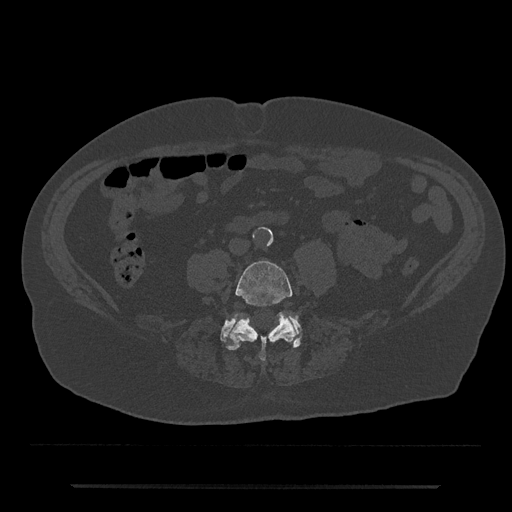
CT including the spine, one axial slice; position 336 of 797 along the scan axis; reconstruction kernel Br40s/3; bone window (W 1800 / L 400 HU); 0.5 mm slice thickness; 512 × 512 image matrix, field of view 434 × 434 mm. Male patient, age 80 years. Case-level facts recorded for this patient, not image findings: primary cancer: prostate; vertebrae with lytic lesions (as recorded): L1, T11.
Outlined on this slice (semi-automatically segmented with operator editing):
- L4 vertebra: bounding box [x1, y1, x2, y2] px = [227, 260, 297, 361]
- L5 vertebra: [220, 314, 302, 350]